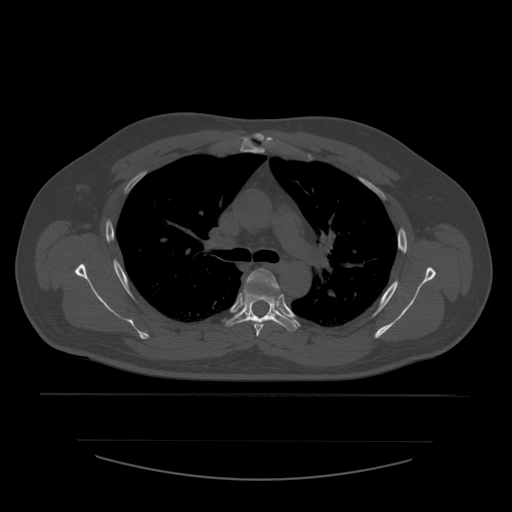
CT including the spine, one axial slice. Position 405 of 532 along the scan axis. Reconstruction kernel STANDARD. Bone window (W 1800 / L 400 HU). 1.25 mm slice thickness. 512 × 512 image matrix. Patient age 44 years. Case-level facts recorded for this patient, not image findings: primary cancer: soft tissue sarcoma.
Outlined on this slice (semi-automatic segmentation, software-assisted and operator-edited):
- T4 vertebra: bounding box [x1, y1, x2, y2] px = [244, 269, 280, 337]
- T5 vertebra: [226, 279, 297, 332]